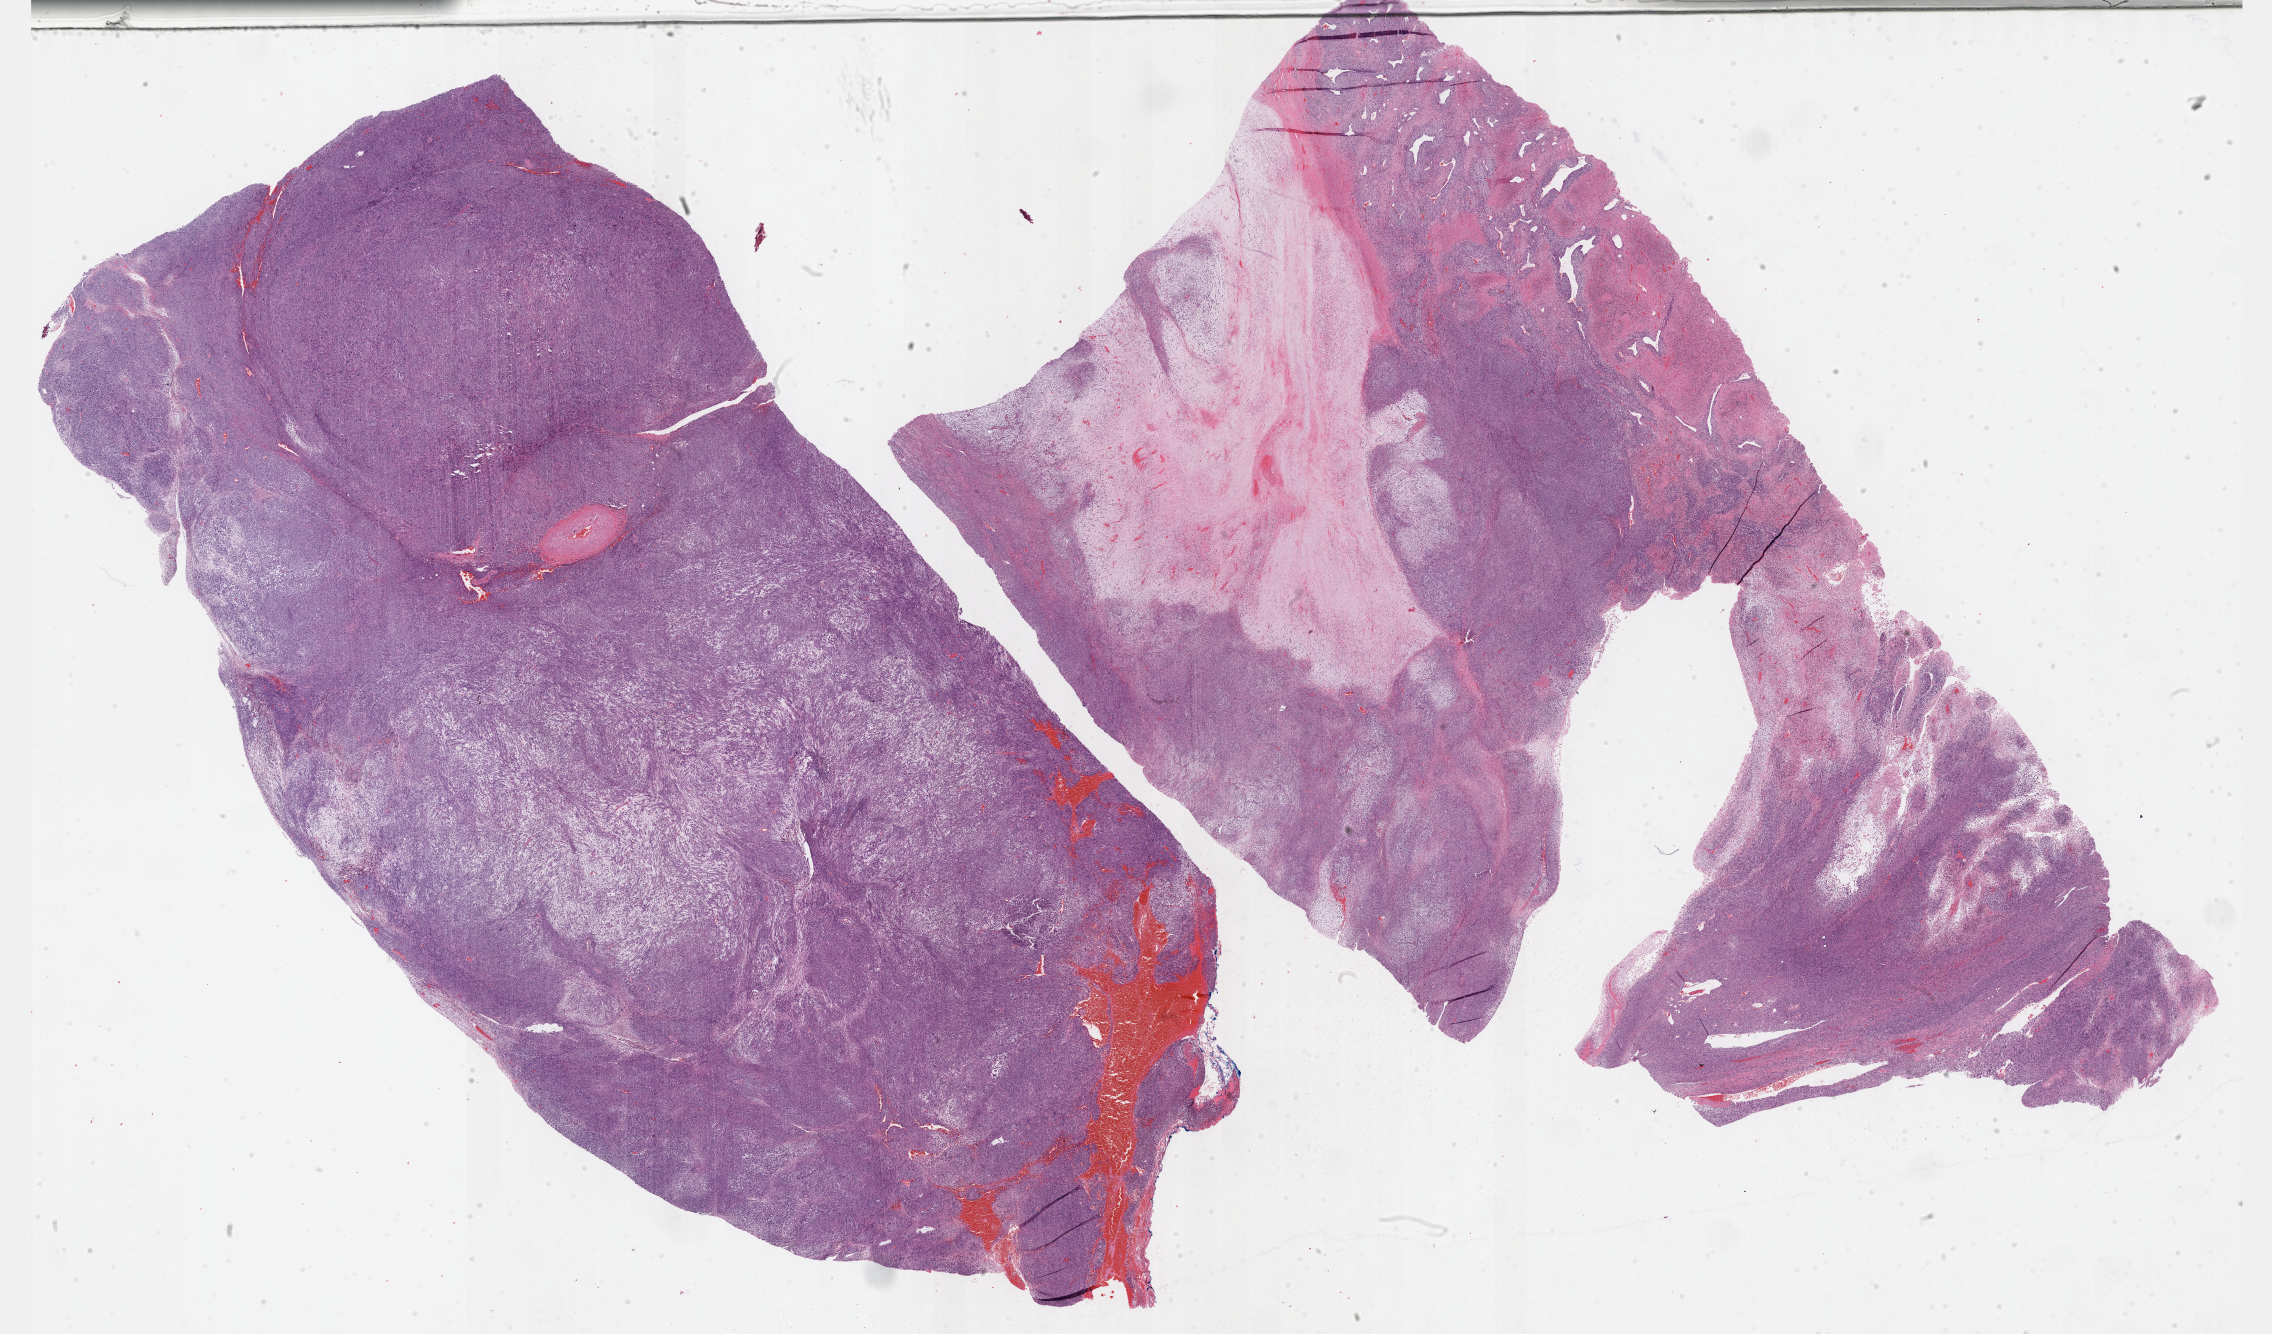
Hematoxylin and eosin (H&E) stained whole-slide image, low-resolution overview of the scanned area, about 36.7 x 21.6 mm; formalin-fixed paraffin-embedded (FFPE) diagnostic section; primary tumour sample from the connective, subcutaneous and other soft tissues. Patient: female, age at initial diagnosis 70 years.
• pathologic diagnosis: Undifferentiated sarcoma